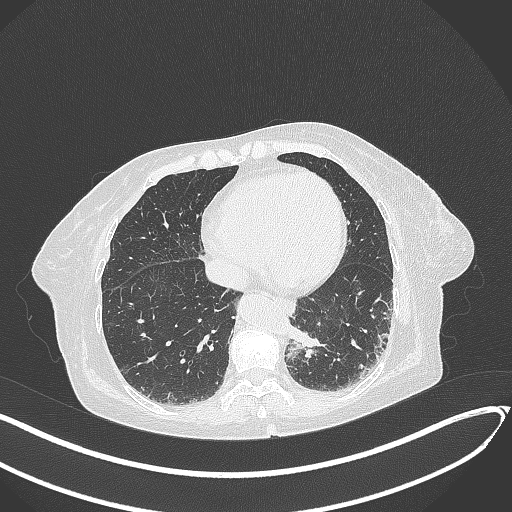
Chest CT, one axial slice. Slice 63 of 324 in the series (ordered by position). Reconstruction kernel B70f. Lung window (W 1500 / L -600 HU). 1 mm slice thickness. 512 × 512 image matrix. Patient: female, 82 years. Case-level facts recorded for this patient, not image findings: clinical TNM (as recorded): T1b N0 M1.
Structures marked on this image (rectangle marked by the reading radiologist):
- lung tumour (recorded histology: adenocarcinoma): bounding box (x1, y1, x2, y2) in pixels: (290, 325, 323, 361)